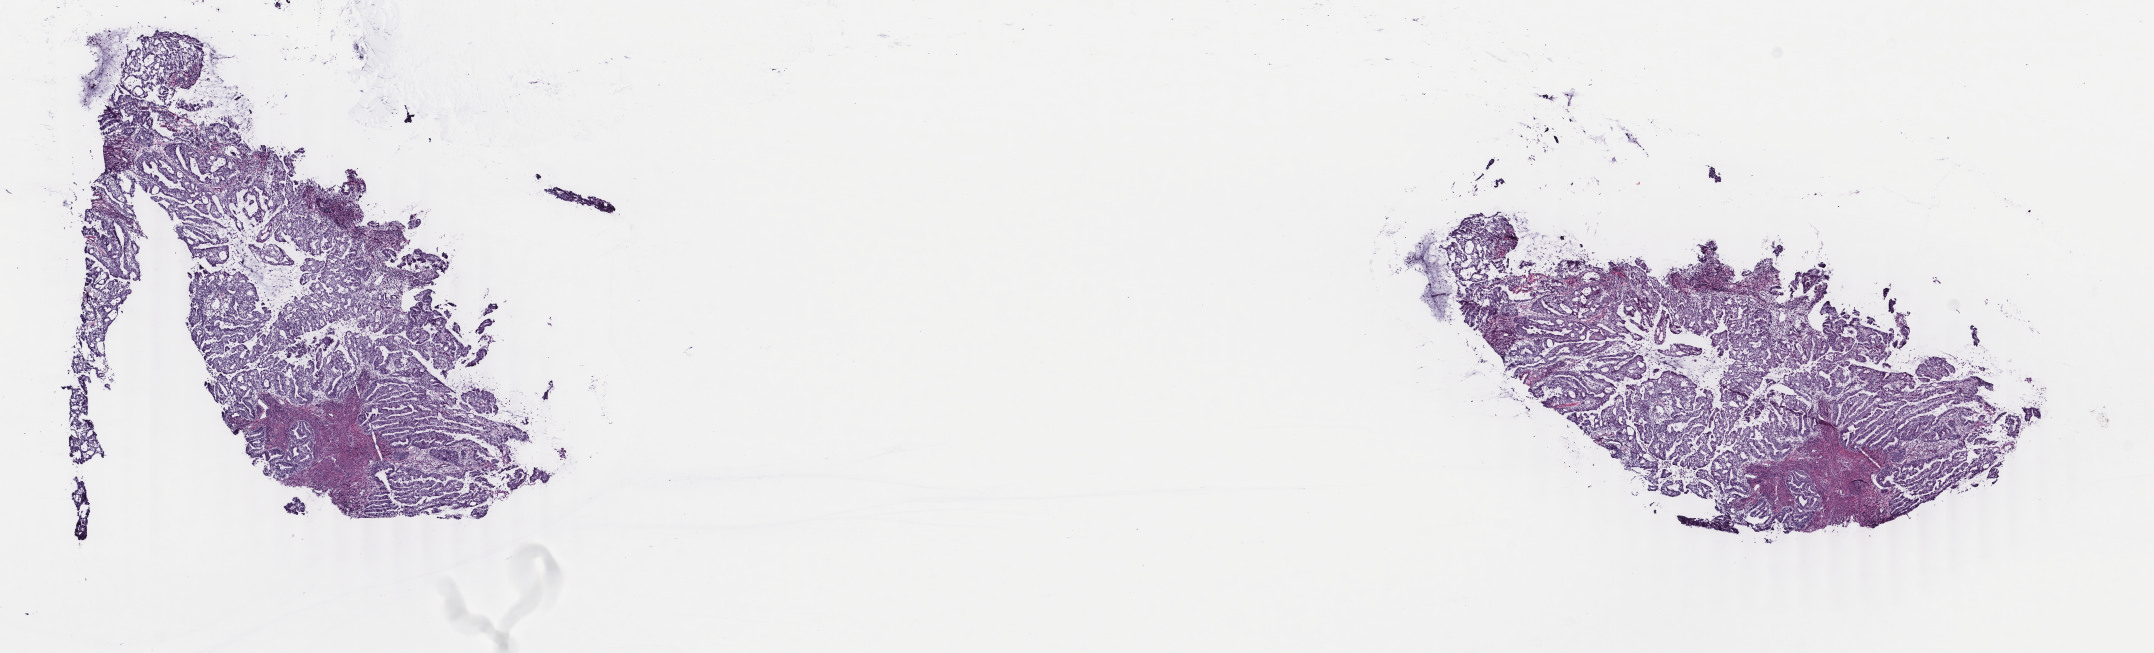
H&E-stained whole-slide image — low-resolution overview of the scanned area, about 17.1 x 5.2 mm. Frozen section from the top of the tissue portion. Uterus, primary tumour sample. Female, age 73 years at initial diagnosis.
Diagnosis: Endometrioid adenocarcinoma, NOS (endometrium).